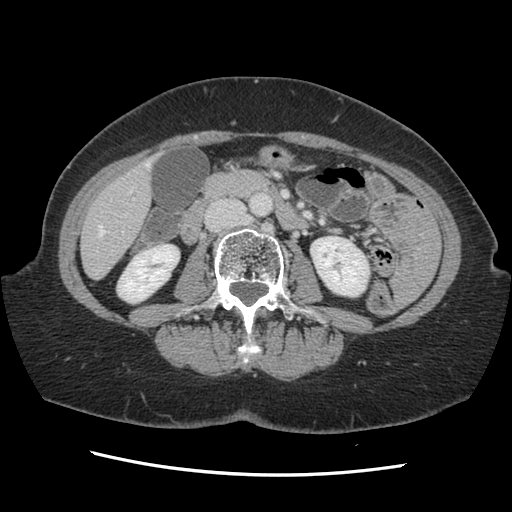
Contrast-enhanced abdominal CT, one axial slice. Position 43 of 141 along the scan axis. Soft-tissue window (W 400 / L 40 HU). 2.5 mm slice thickness. 512 × 512 image matrix, field of view 330 × 330 mm. Female patient, age 61 years. Case-level facts recorded for this patient, not image findings: diagnosis: colorectal cancer liver metastases, imaged before liver resection; multiple liver metastases: no; largest metastasis: 2.4 cm; chemotherapy before resection: no.
Outlined on this slice (manually delineated by an expert):
- hepatic veins: box from (x=96, y=163) to (x=149, y=272) px
- liver: (x=82, y=164)–(x=152, y=278)
- planned liver remnant (the part of the liver to remain after resection): (x=82, y=173)–(x=152, y=278)